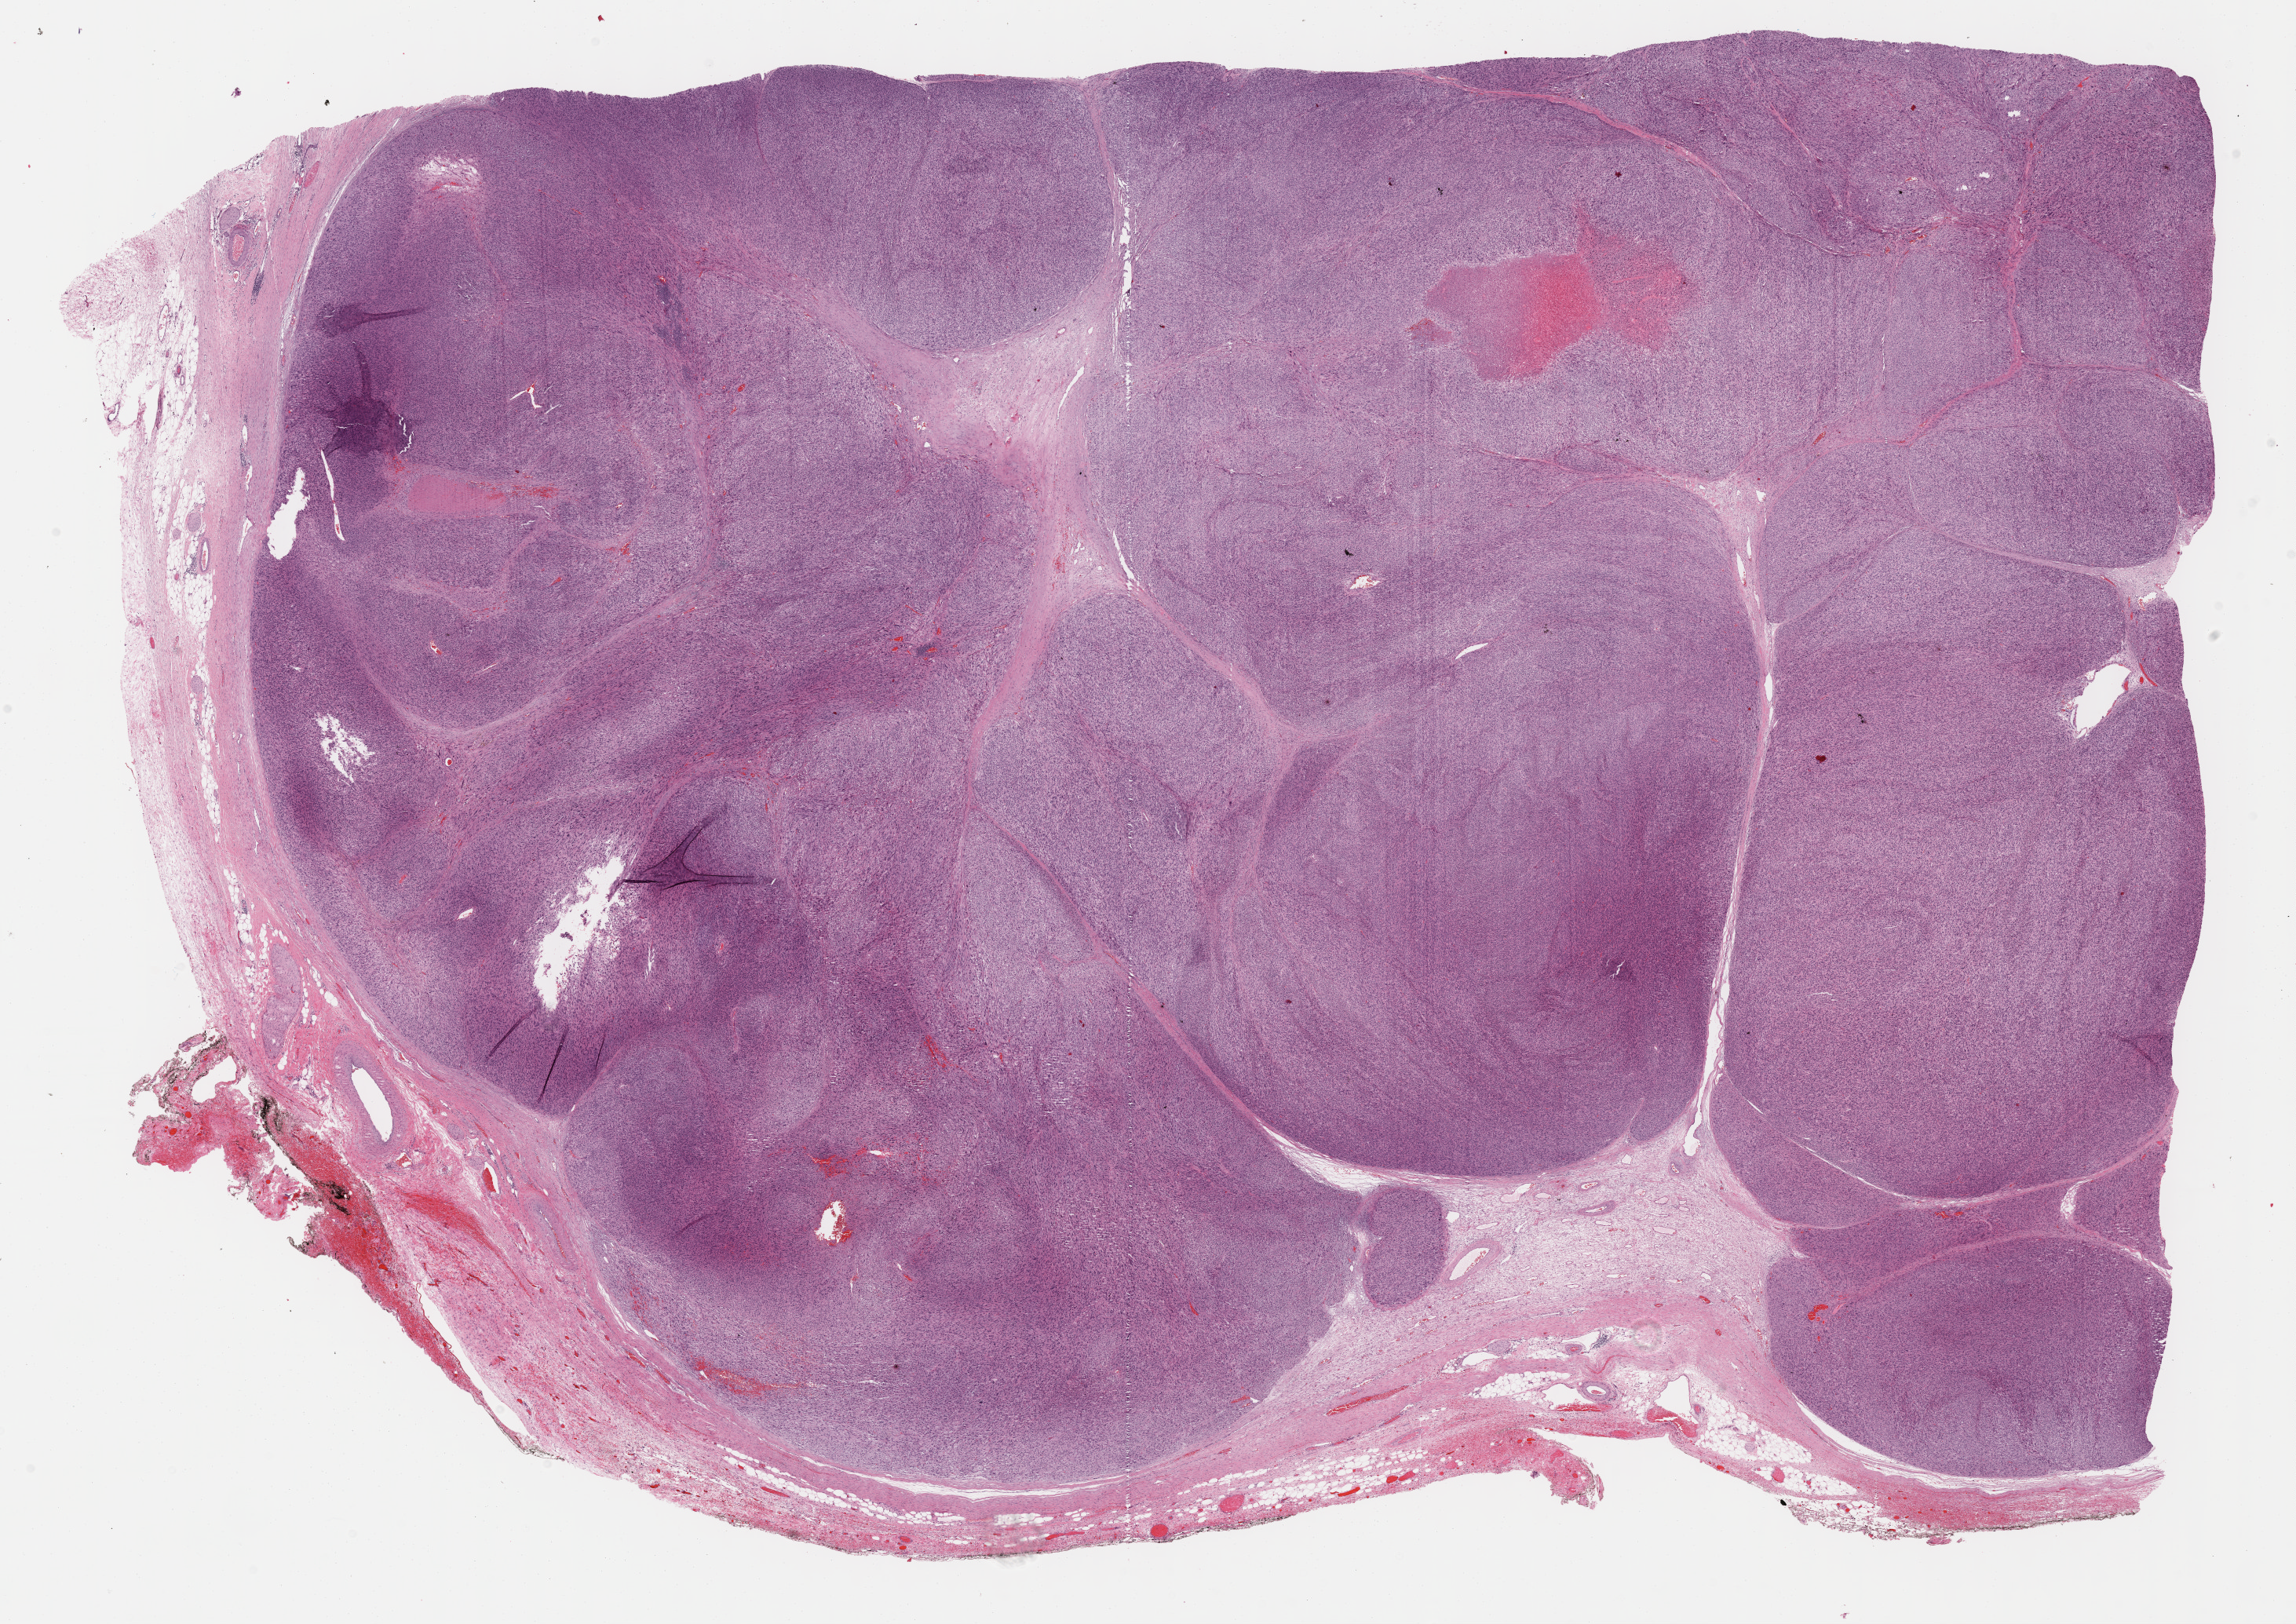
Hematoxylin and eosin (H&E) stained whole-slide image, whole scanned area (about 23.7 x 16.7 mm, slide scanned at 40x) shown as a low-resolution overview, FFPE section, sample: primary tumour, retroperitoneum and peritoneum. Male patient; age at initial diagnosis 56 years.
Pathologic diagnosis: Leiomyosarcoma, NOS.